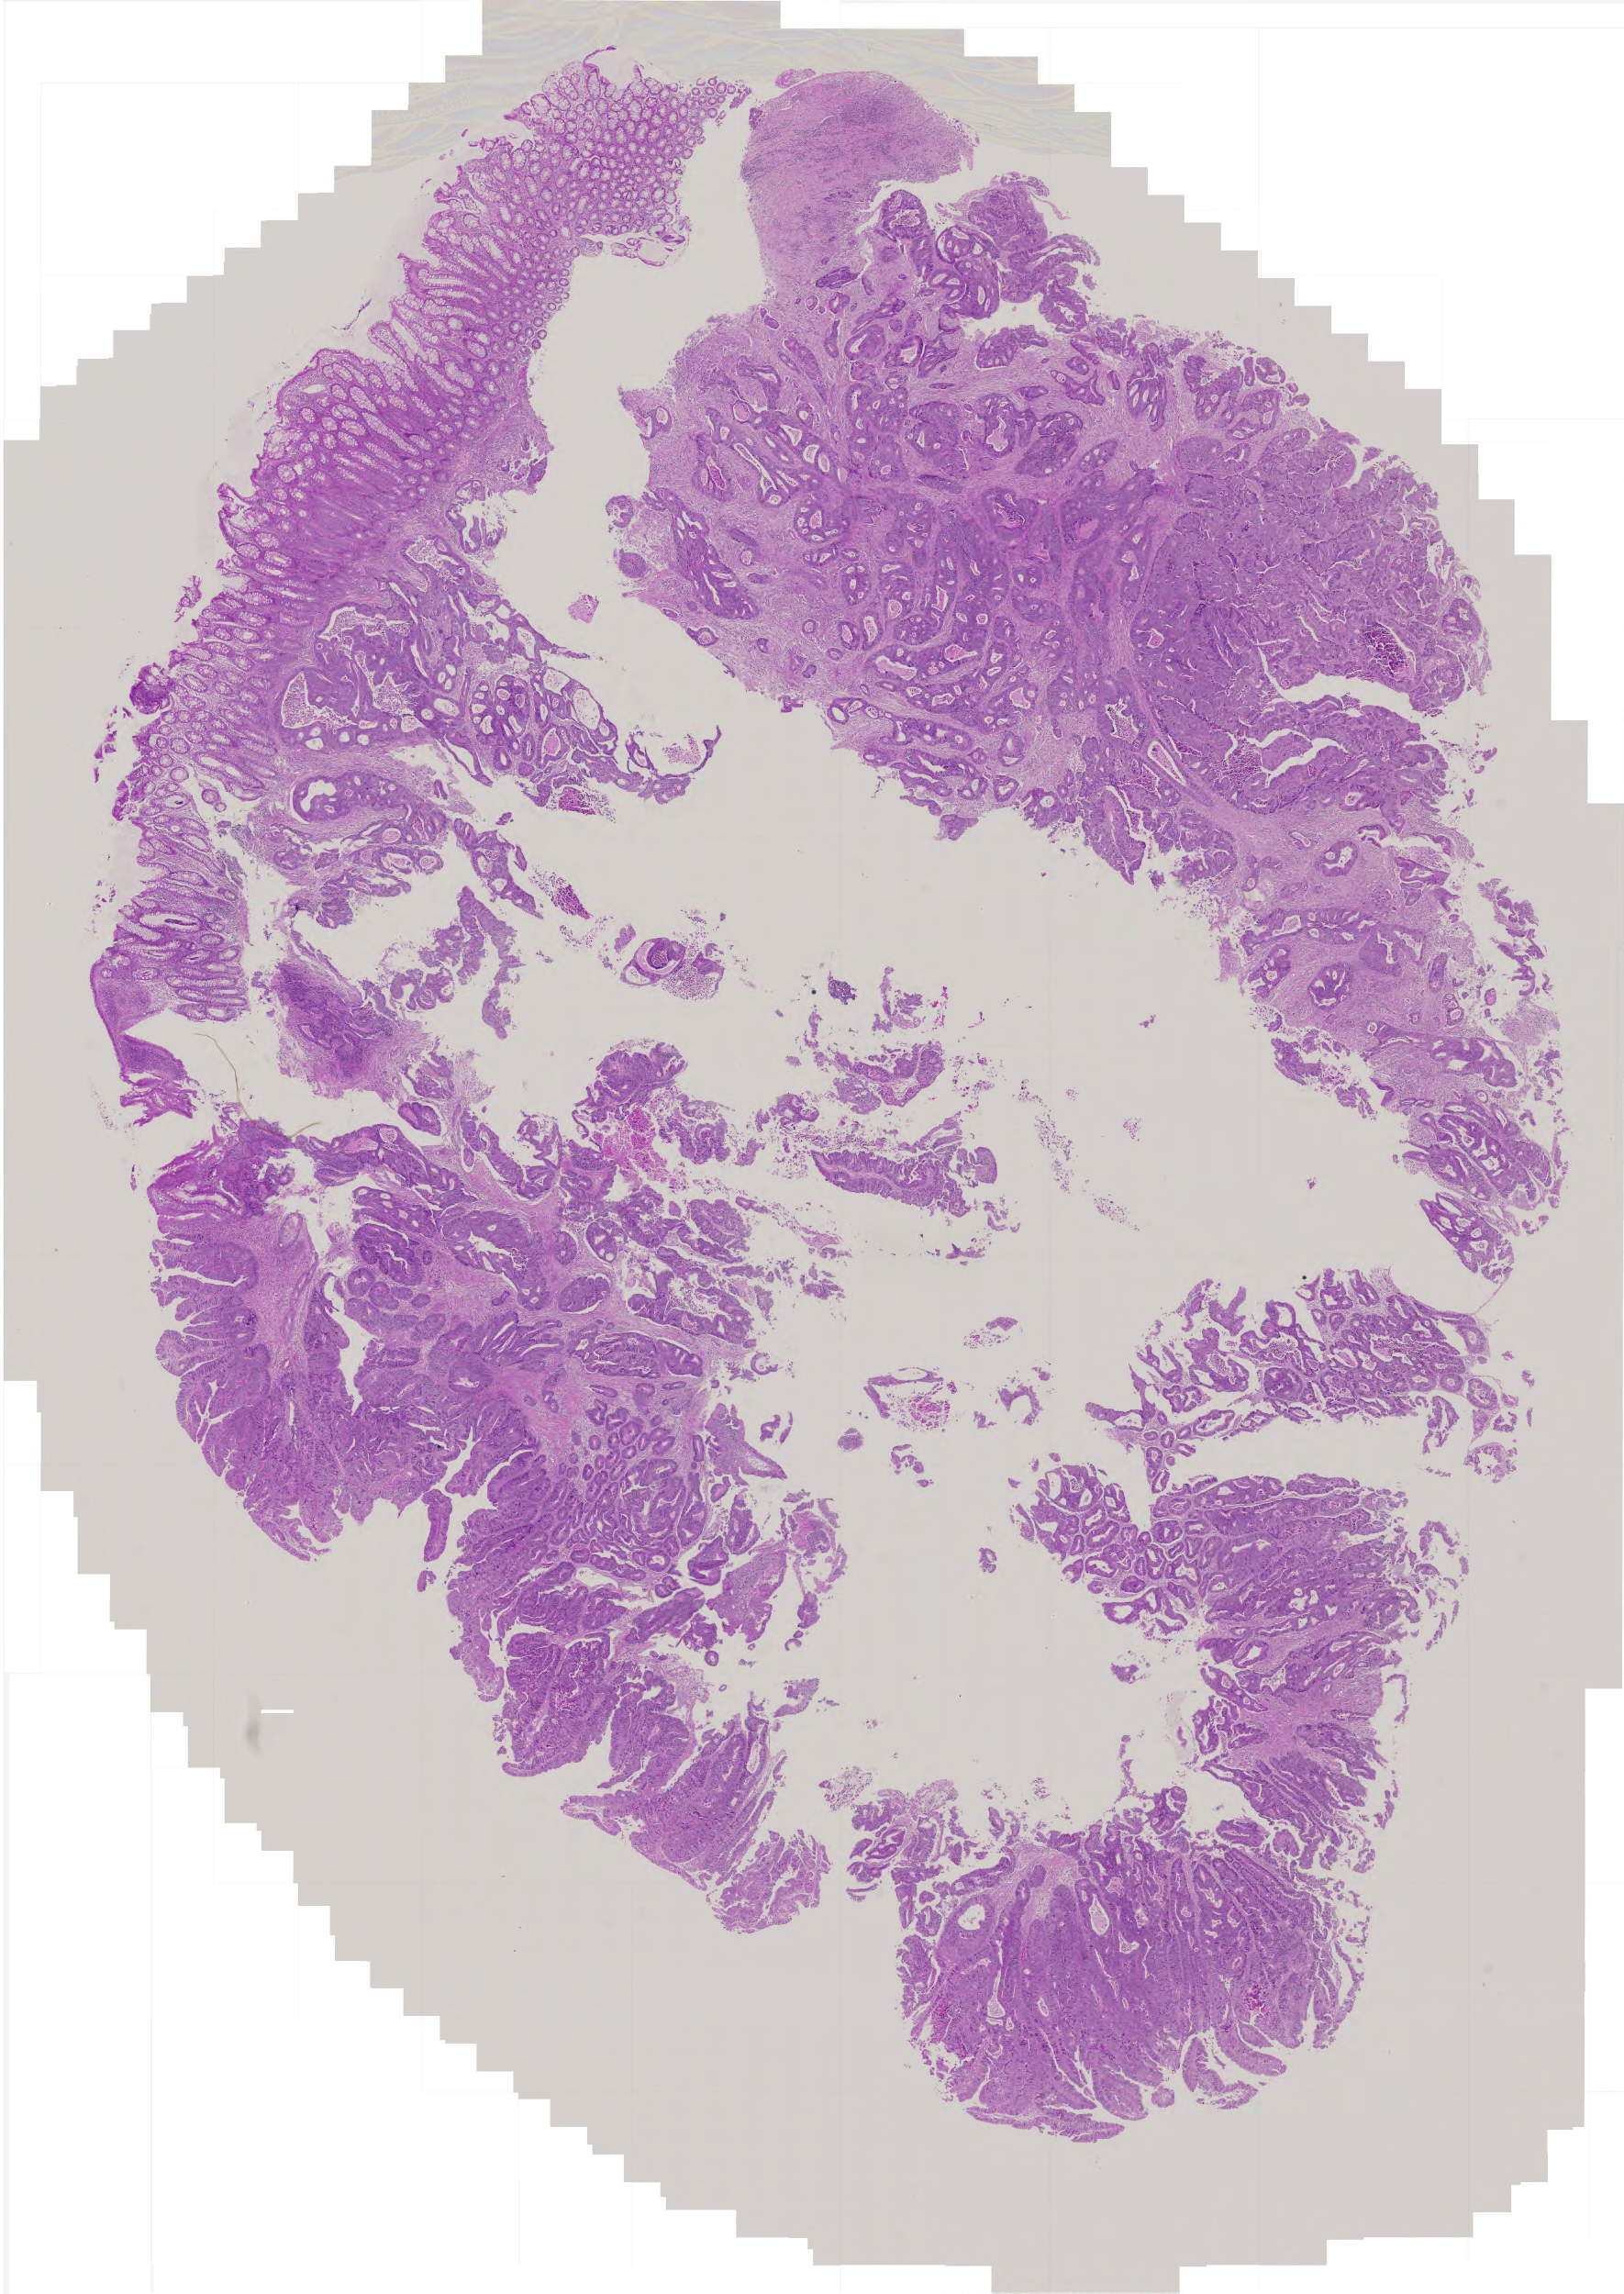
H&E-stained whole-slide image — low-resolution overview of the scanned area, about 3.5 x 5.0 mm, formalin-fixed paraffin-embedded (FFPE) diagnostic section, sample: primary tumour, colon. Male patient; age at initial diagnosis 77 years.
Histologic diagnosis: Adenocarcinoma, NOS. AJCC pathologic stage: II (5th edition).